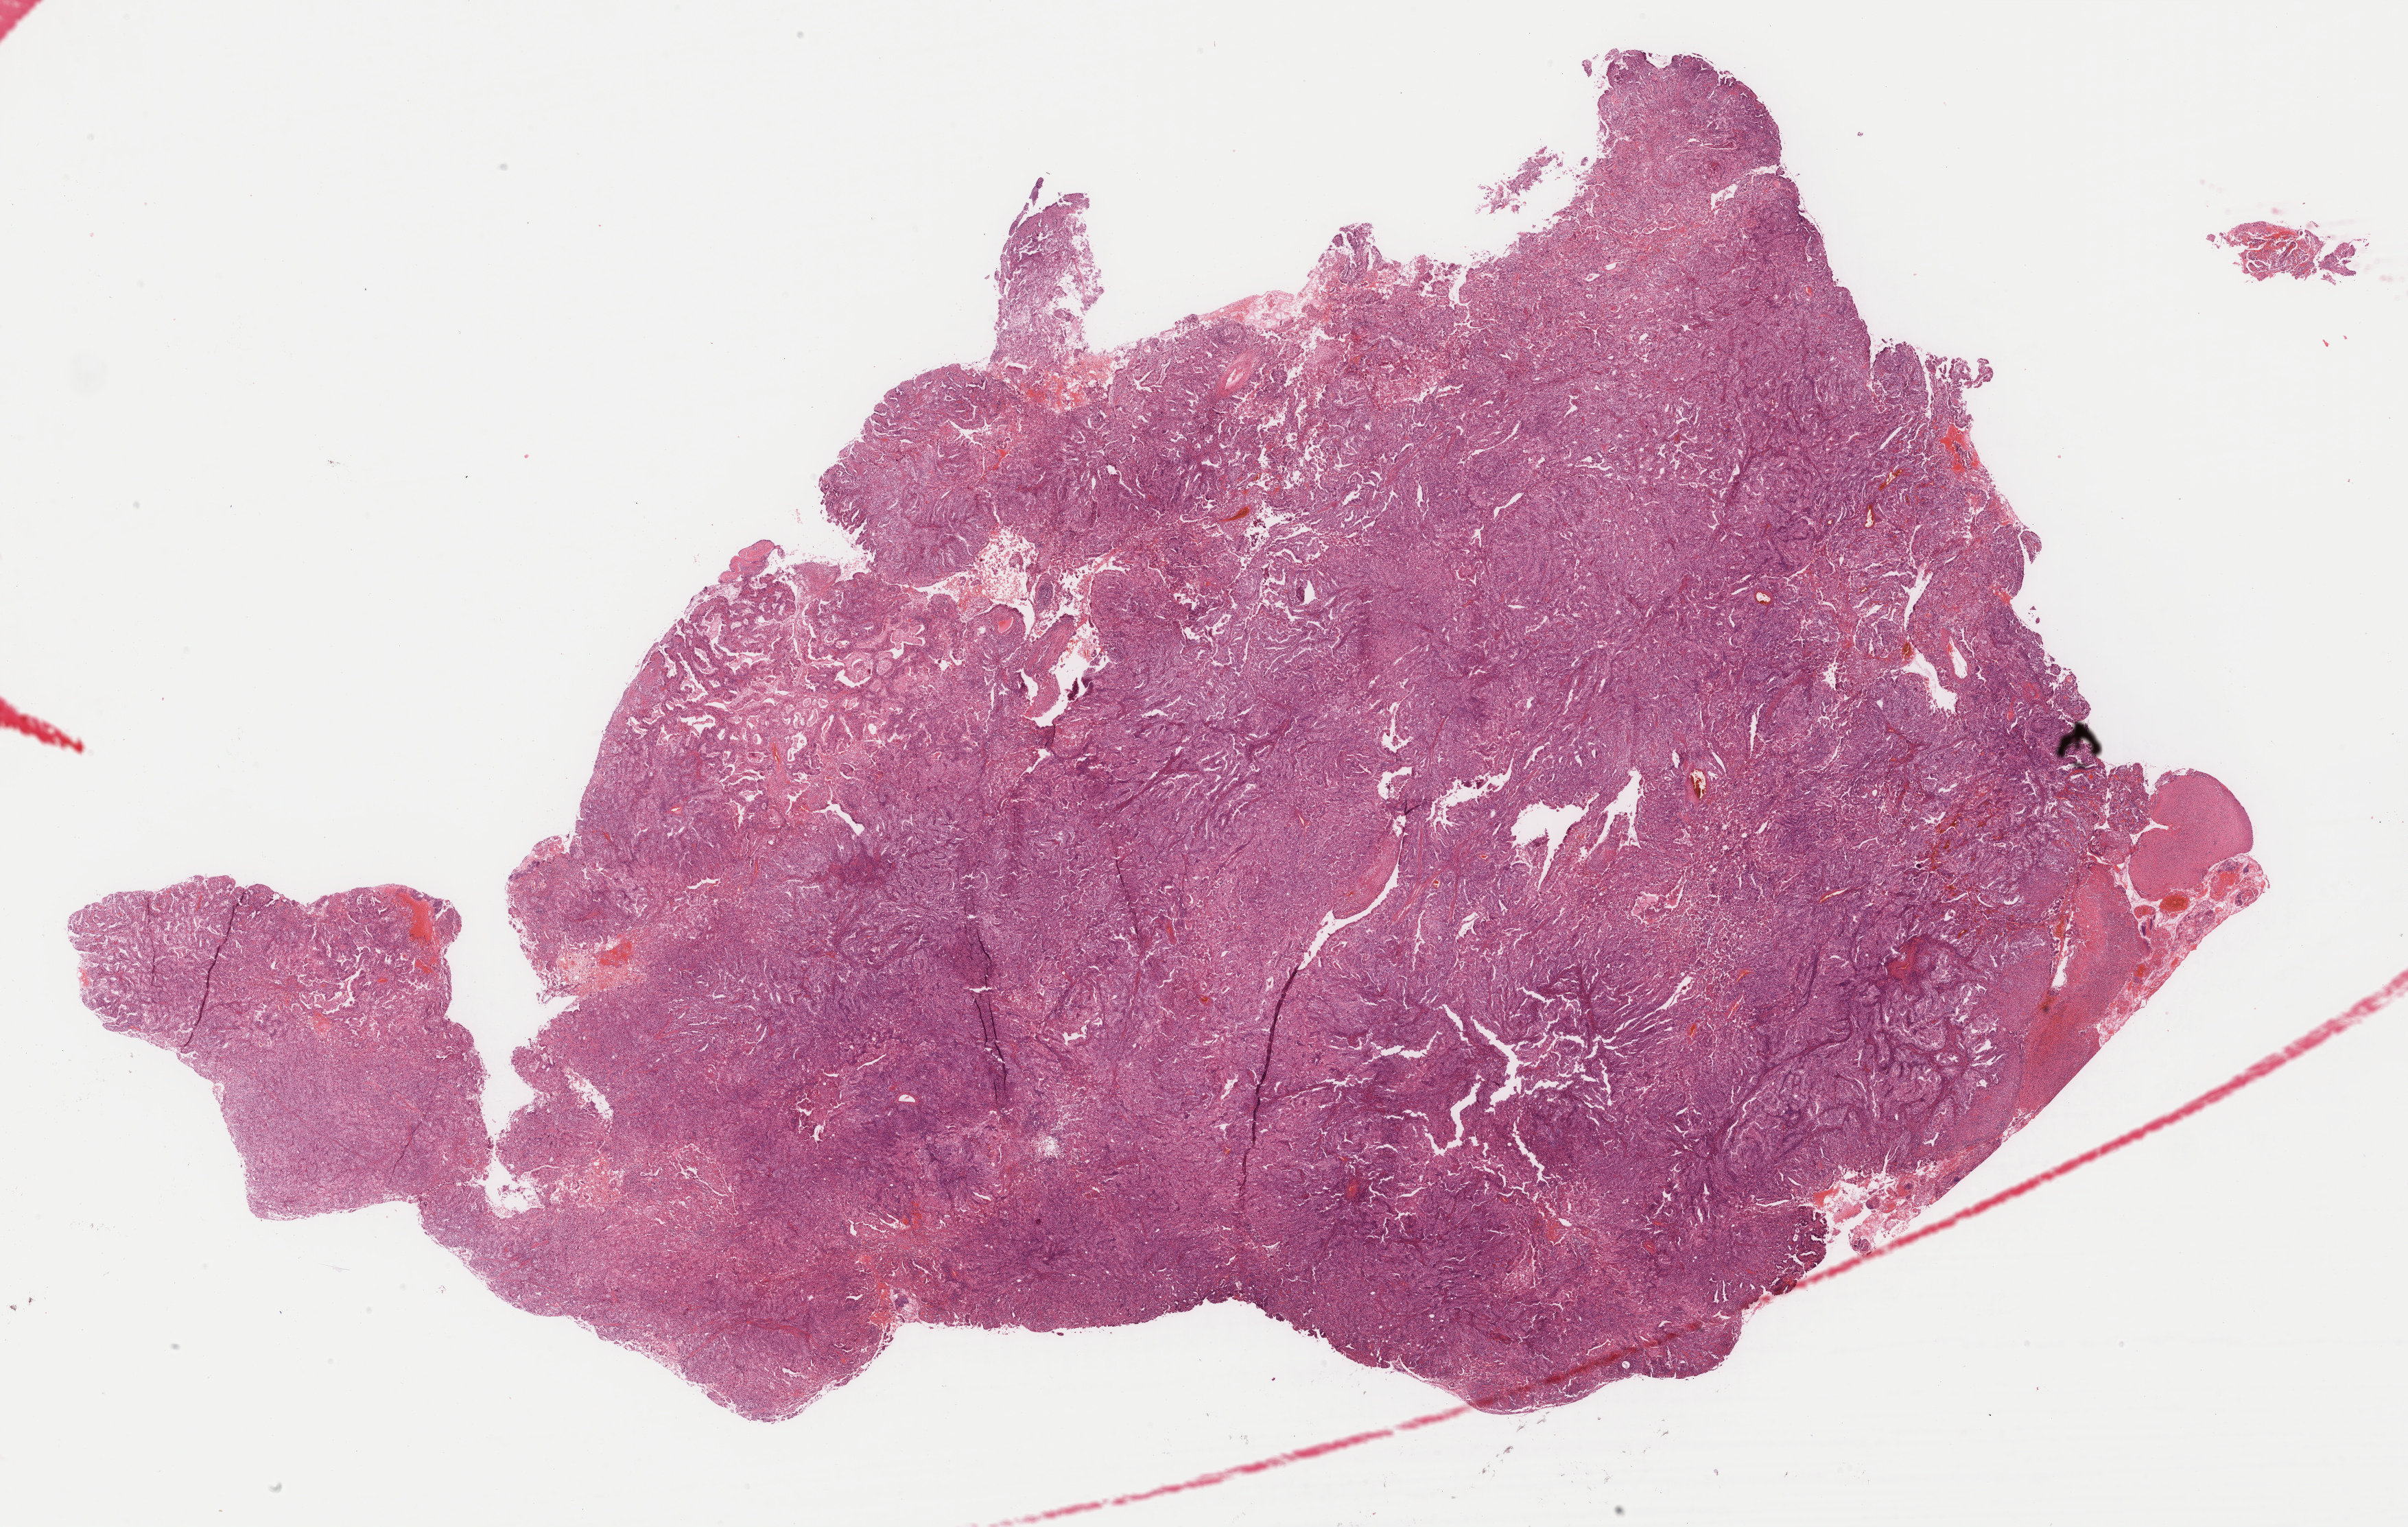
H&E whole-slide image — whole scanned area (about 27.9 x 17.7 mm, slide scanned at 40x) shown as a low-resolution overview. Formalin-fixed paraffin-embedded (FFPE) diagnostic section. Primary tumour sample from the stomach. Patient: female, age at initial diagnosis 72 years. Histologic grade: G3 (poorly differentiated).
• diagnosis: Adenocarcinoma, NOS
• AJCC pathologic stage: IIB (7th edition)
• lymph nodes positive (case pathology): 0 of 11 examined